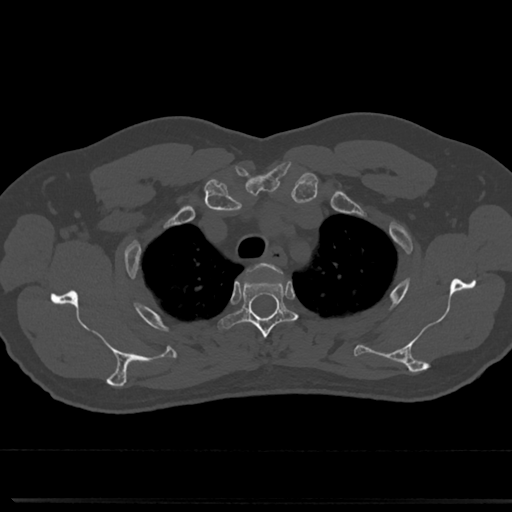
CT including the spine, one axial slice. Slice 597 of 817 in the series (ordered by position). 120 kVp. Bone window (W 1800 / L 400 HU). 0.5 mm slice thickness. 512 × 512 image matrix, field of view 355 × 355 mm. Male patient, age 61 years. From the clinical record (not read from this slice): primary cancer: prostate.
Annotated regions visible in this slice (semi-automatically segmented with operator editing):
- T3 vertebra: bounding box [x1, y1, x2, y2] px = [228, 267, 294, 346]